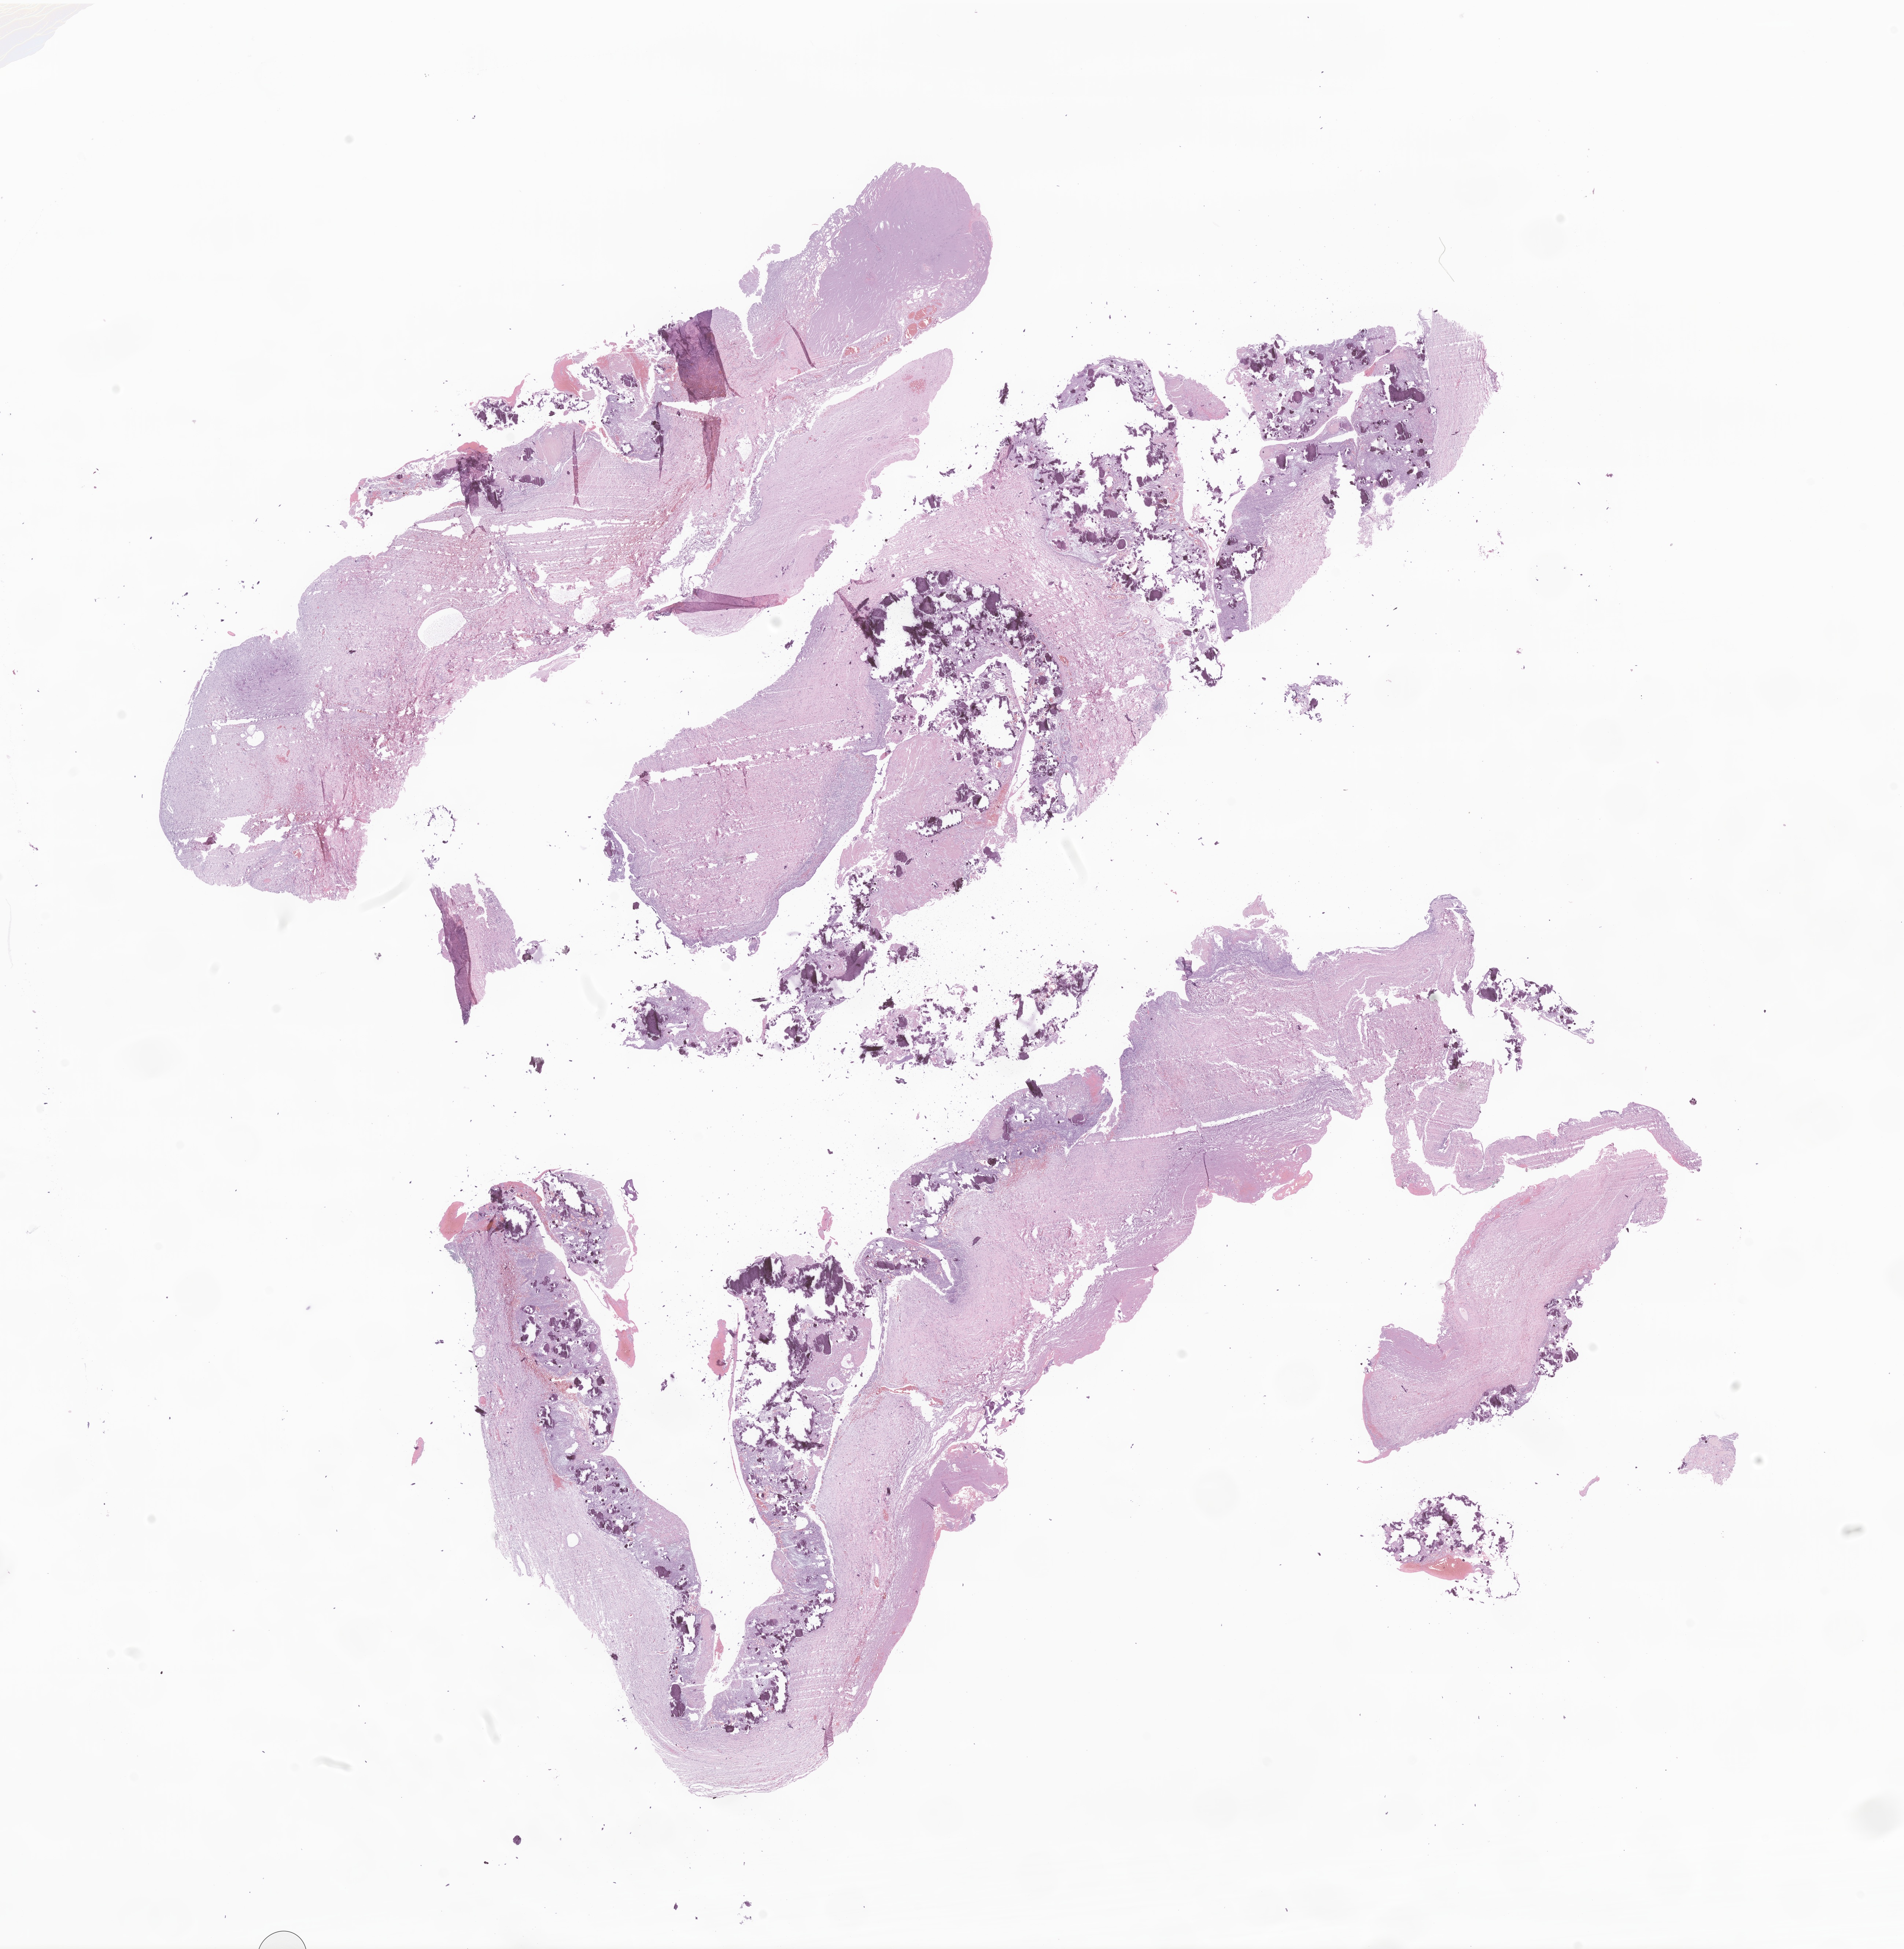
Haematoxylin and eosin whole-slide image of tumor tissue from the frontal lobe, low-resolution overview of the scanned area, about 21.9 x 22.4 mm, FFPE section. Patient male; age 77 months (6 years 5 months).
Recorded diagnosis: Craniopharyngioma, NOS.